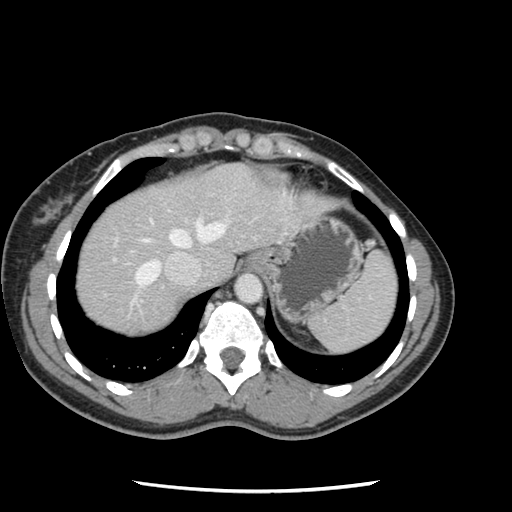
Contrast-enhanced abdominal CT, one axial slice. 120 kVp. Intravenous contrast given. Soft-tissue window (W 400 / L 40 HU). 2.5 mm slice thickness. 512 × 512 image matrix, field of view 330 × 330 mm. Female patient, age 43 years. From the clinical record (not read from this slice): diagnosis: colorectal cancer liver metastases, imaged before liver resection; multiple liver metastases: yes; largest metastasis: 3.4 cm; chemotherapy before resection: no.
Outlined on this slice (expert manual segmentation):
- hepatic veins: bounding box <134,219,227,288> (left, top, right, bottom; pixels)
- liver: <76,163,301,332>
- planned liver remnant (the part of the liver to remain after resection): <76,180,199,305>
- portal vein (with intrahepatic branches): <113,238,134,262>